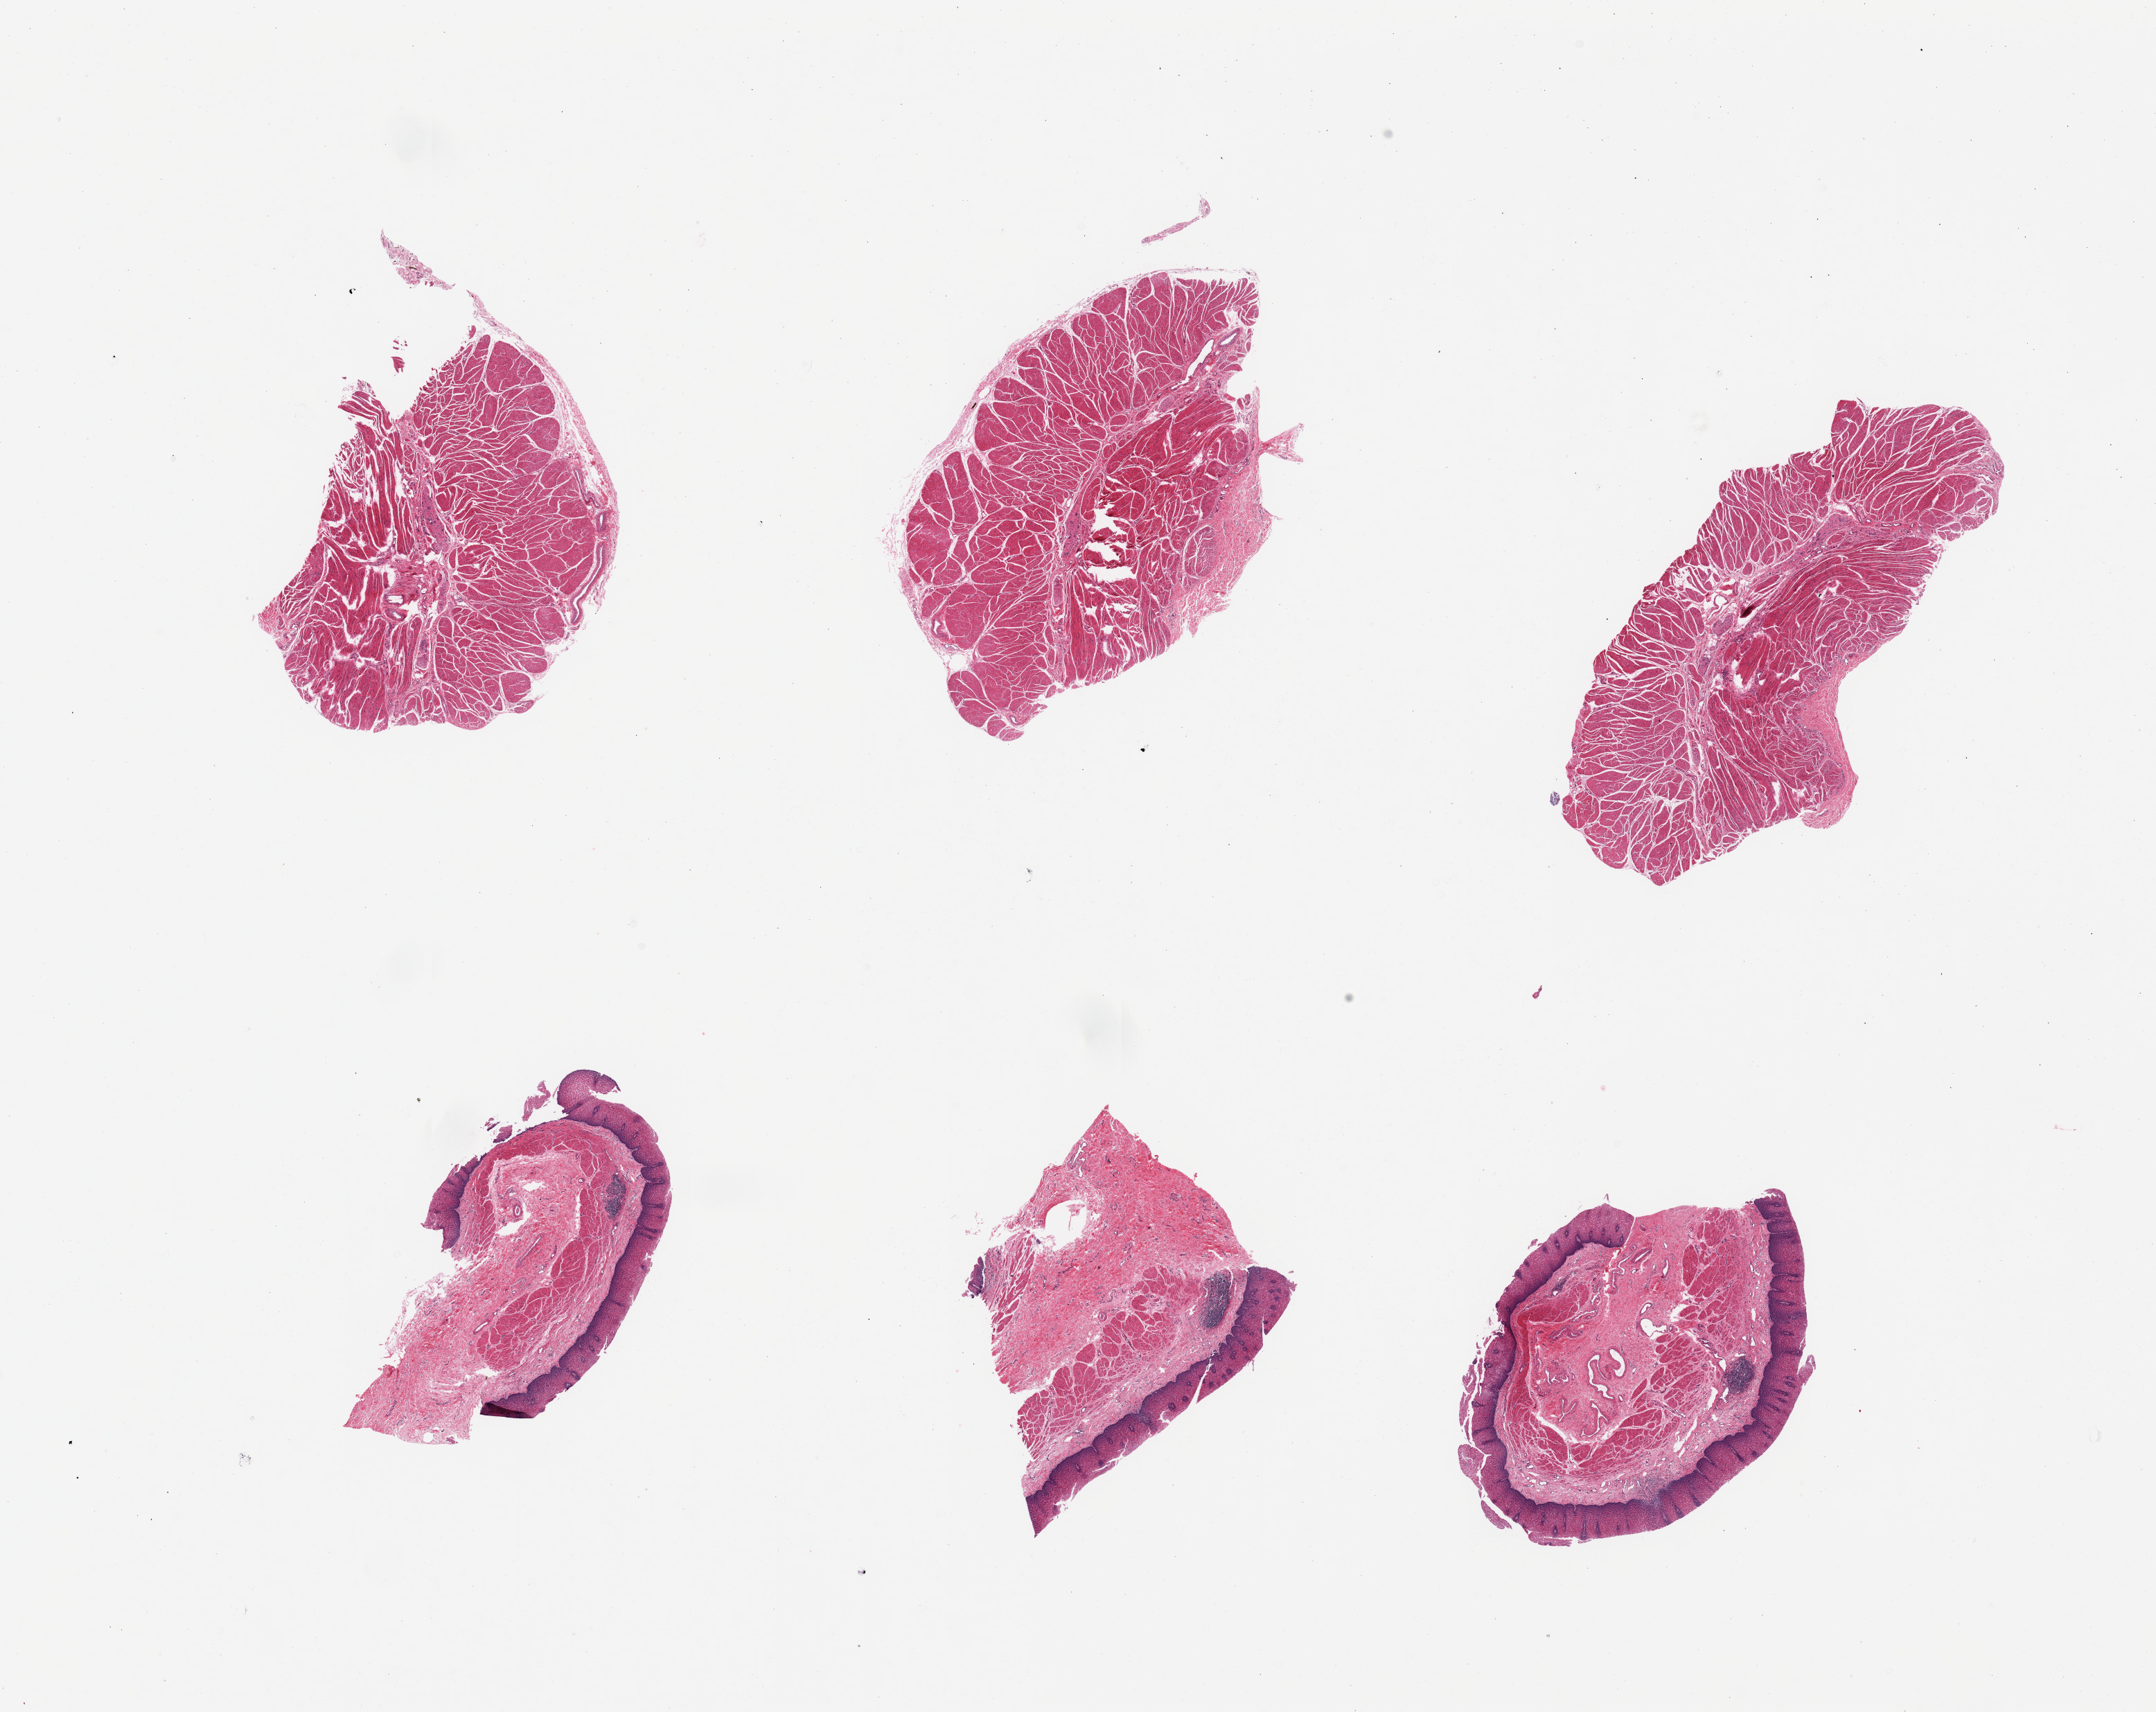
Haematoxylin and eosin whole-slide image, whole scanned area (about 24.6 x 19.5 mm, slide scanned at 20x) shown as a low-resolution overview; PAXgene-fixed paraffin-embedded (PFPE) section; sampled site (target tissue): esophageal muscle; donor tissue sample.
Review note (as recorded): 6 pieces; target muscularis; 3 pieces contain esophageal mucosa.